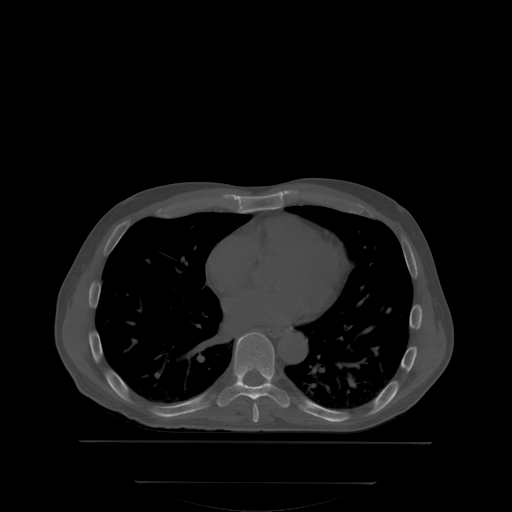
CT including the spine, one axial slice. Slice 216 of 350 in the series (ordered by position). Bone window (W 1800 / L 400 HU). 2.5 mm slice thickness. 512 × 512 image matrix, field of view 500 × 500 mm. Patient: male, 58 years. Case-level facts recorded for this patient, not image findings: primary cancer: prostate; vertebrae with lytic lesions (as recorded): L1.
Outlined on this slice (semi-automatically segmented with operator editing):
- T7 vertebra: bounding box (x1, y1, x2, y2) in pixels: (252, 405, 259, 421)
- T8 vertebra: (216, 332, 290, 407)